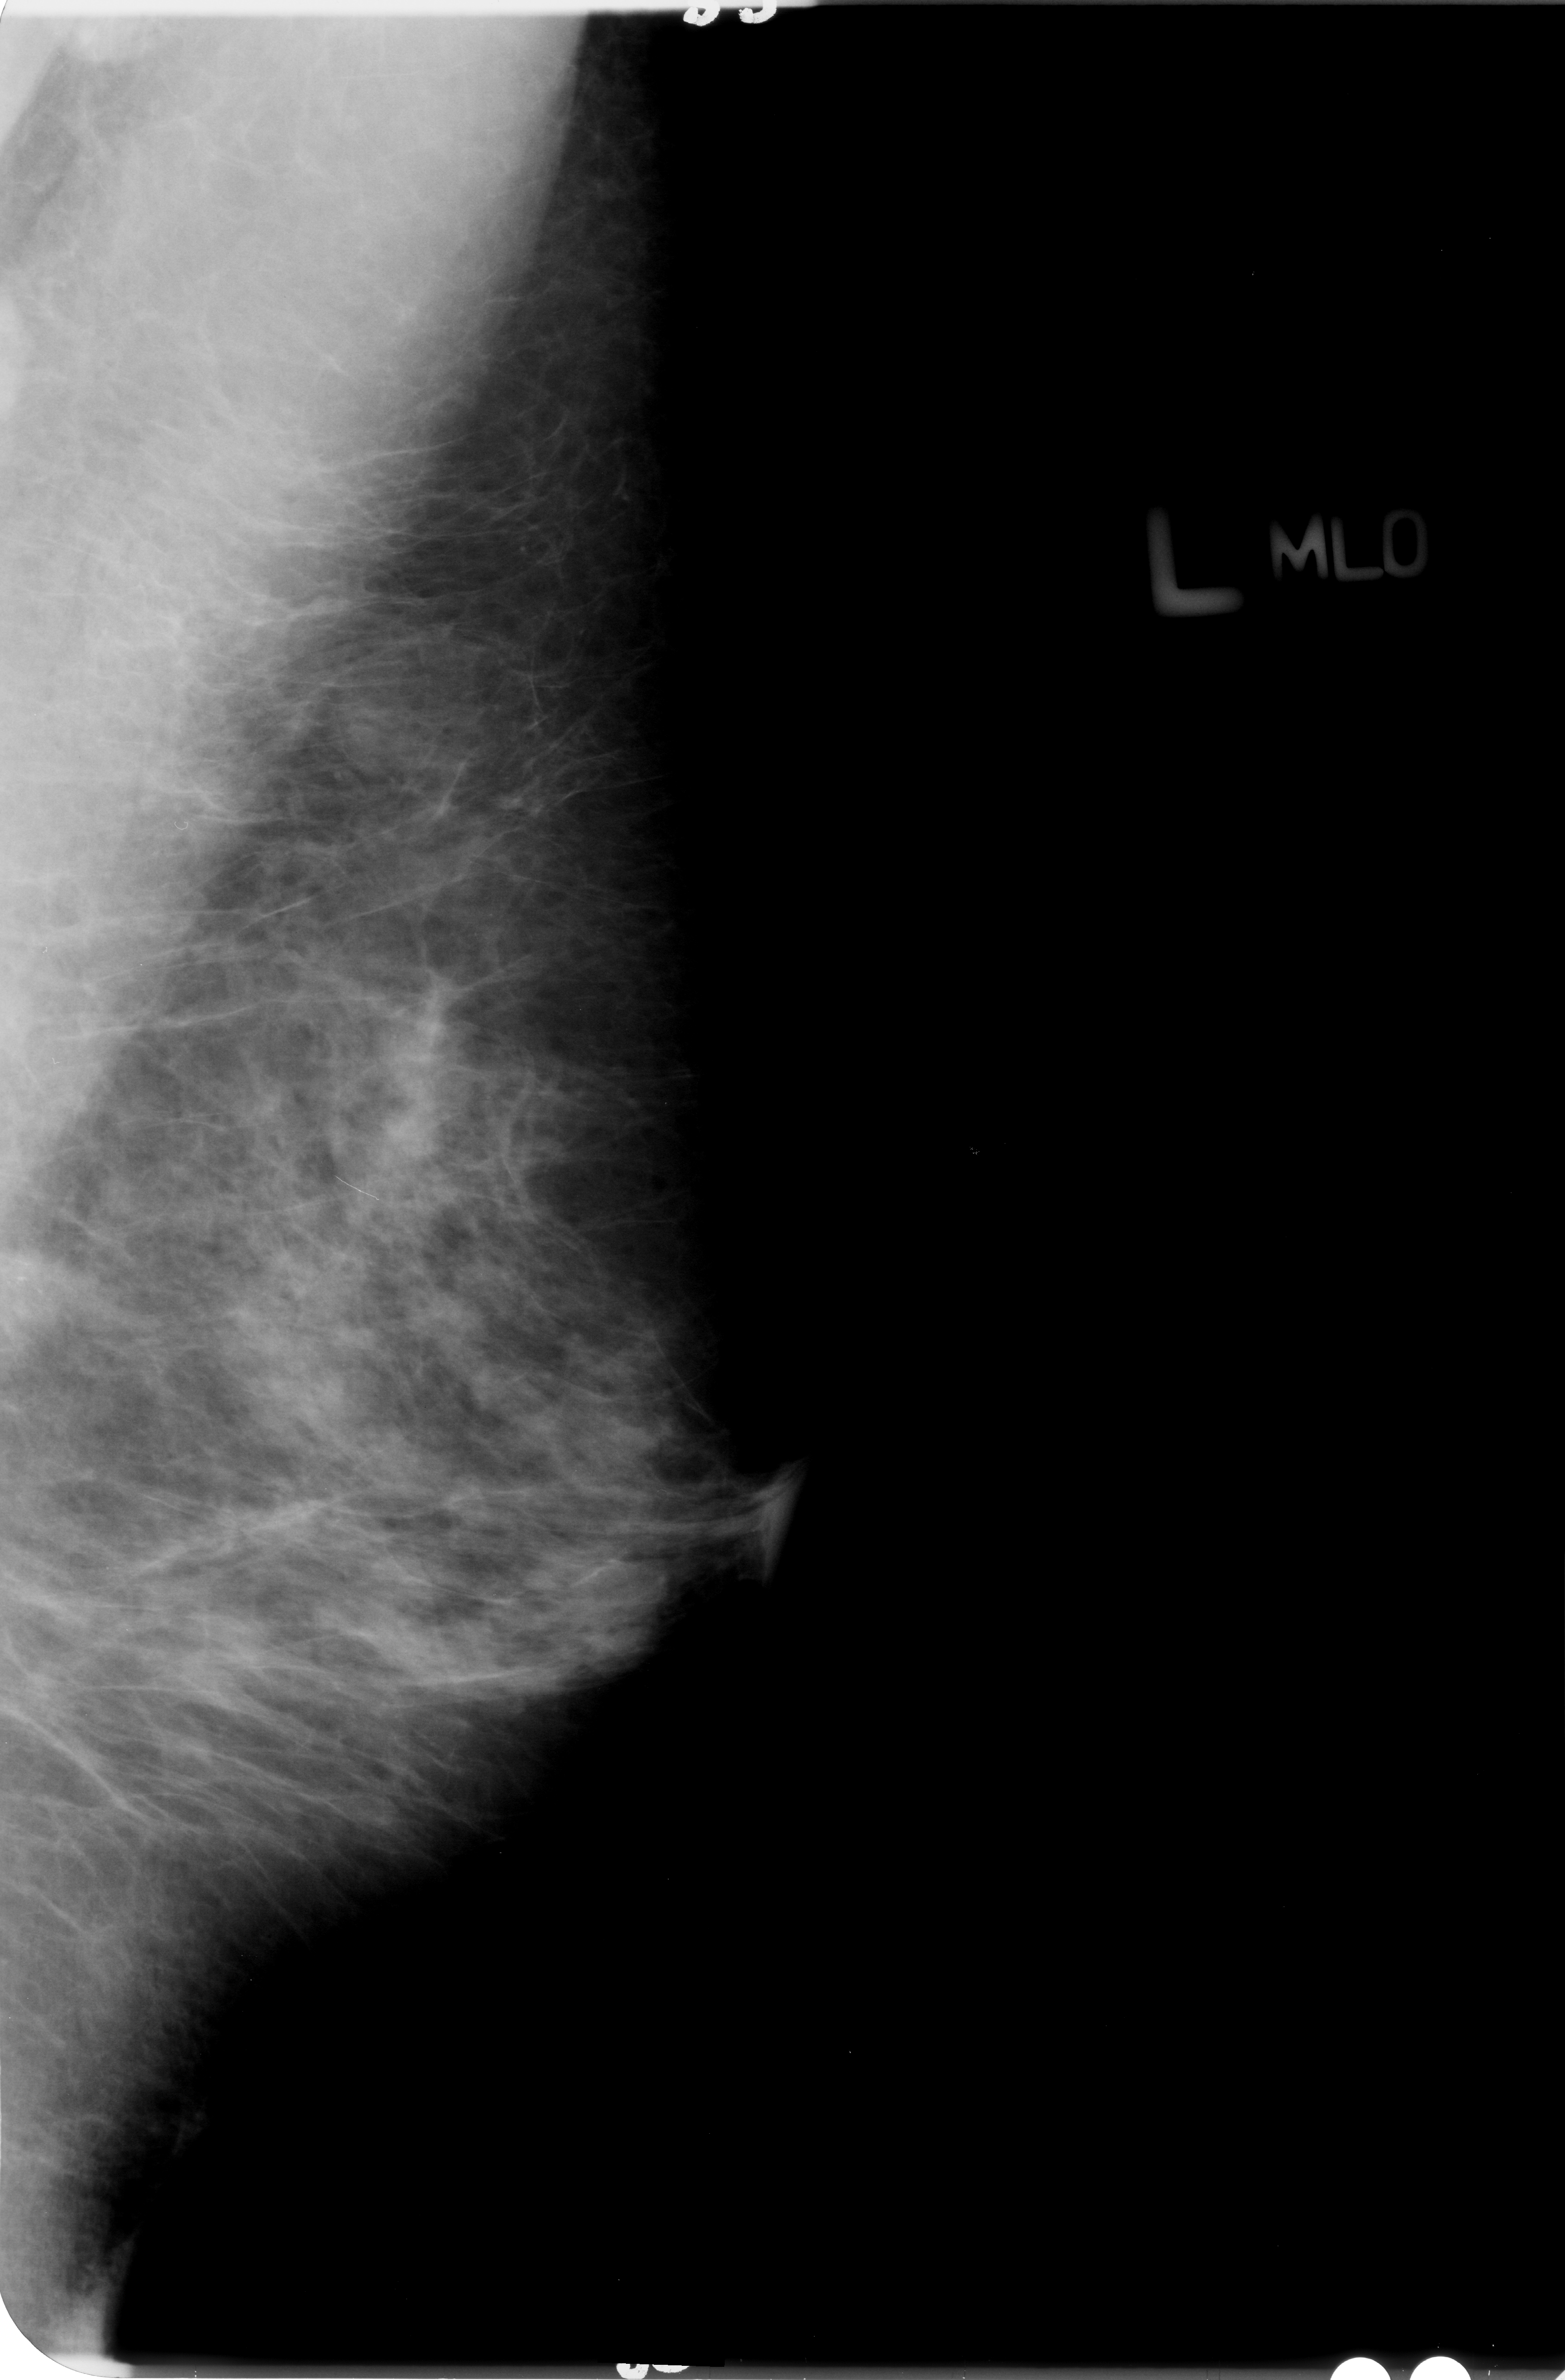
Mammogram (digitized film); left breast; MLO view; breast composition: heterogeneously dense (BI-RADS density category 3 of 4).
- Marked findings (only marked abnormalities are described; nothing is implied about the rest of the image): calcifications, morphology amorphous / pleomorphic, distribution clustered; BI-RADS assessment category 4; pathology (as recorded): malignant.